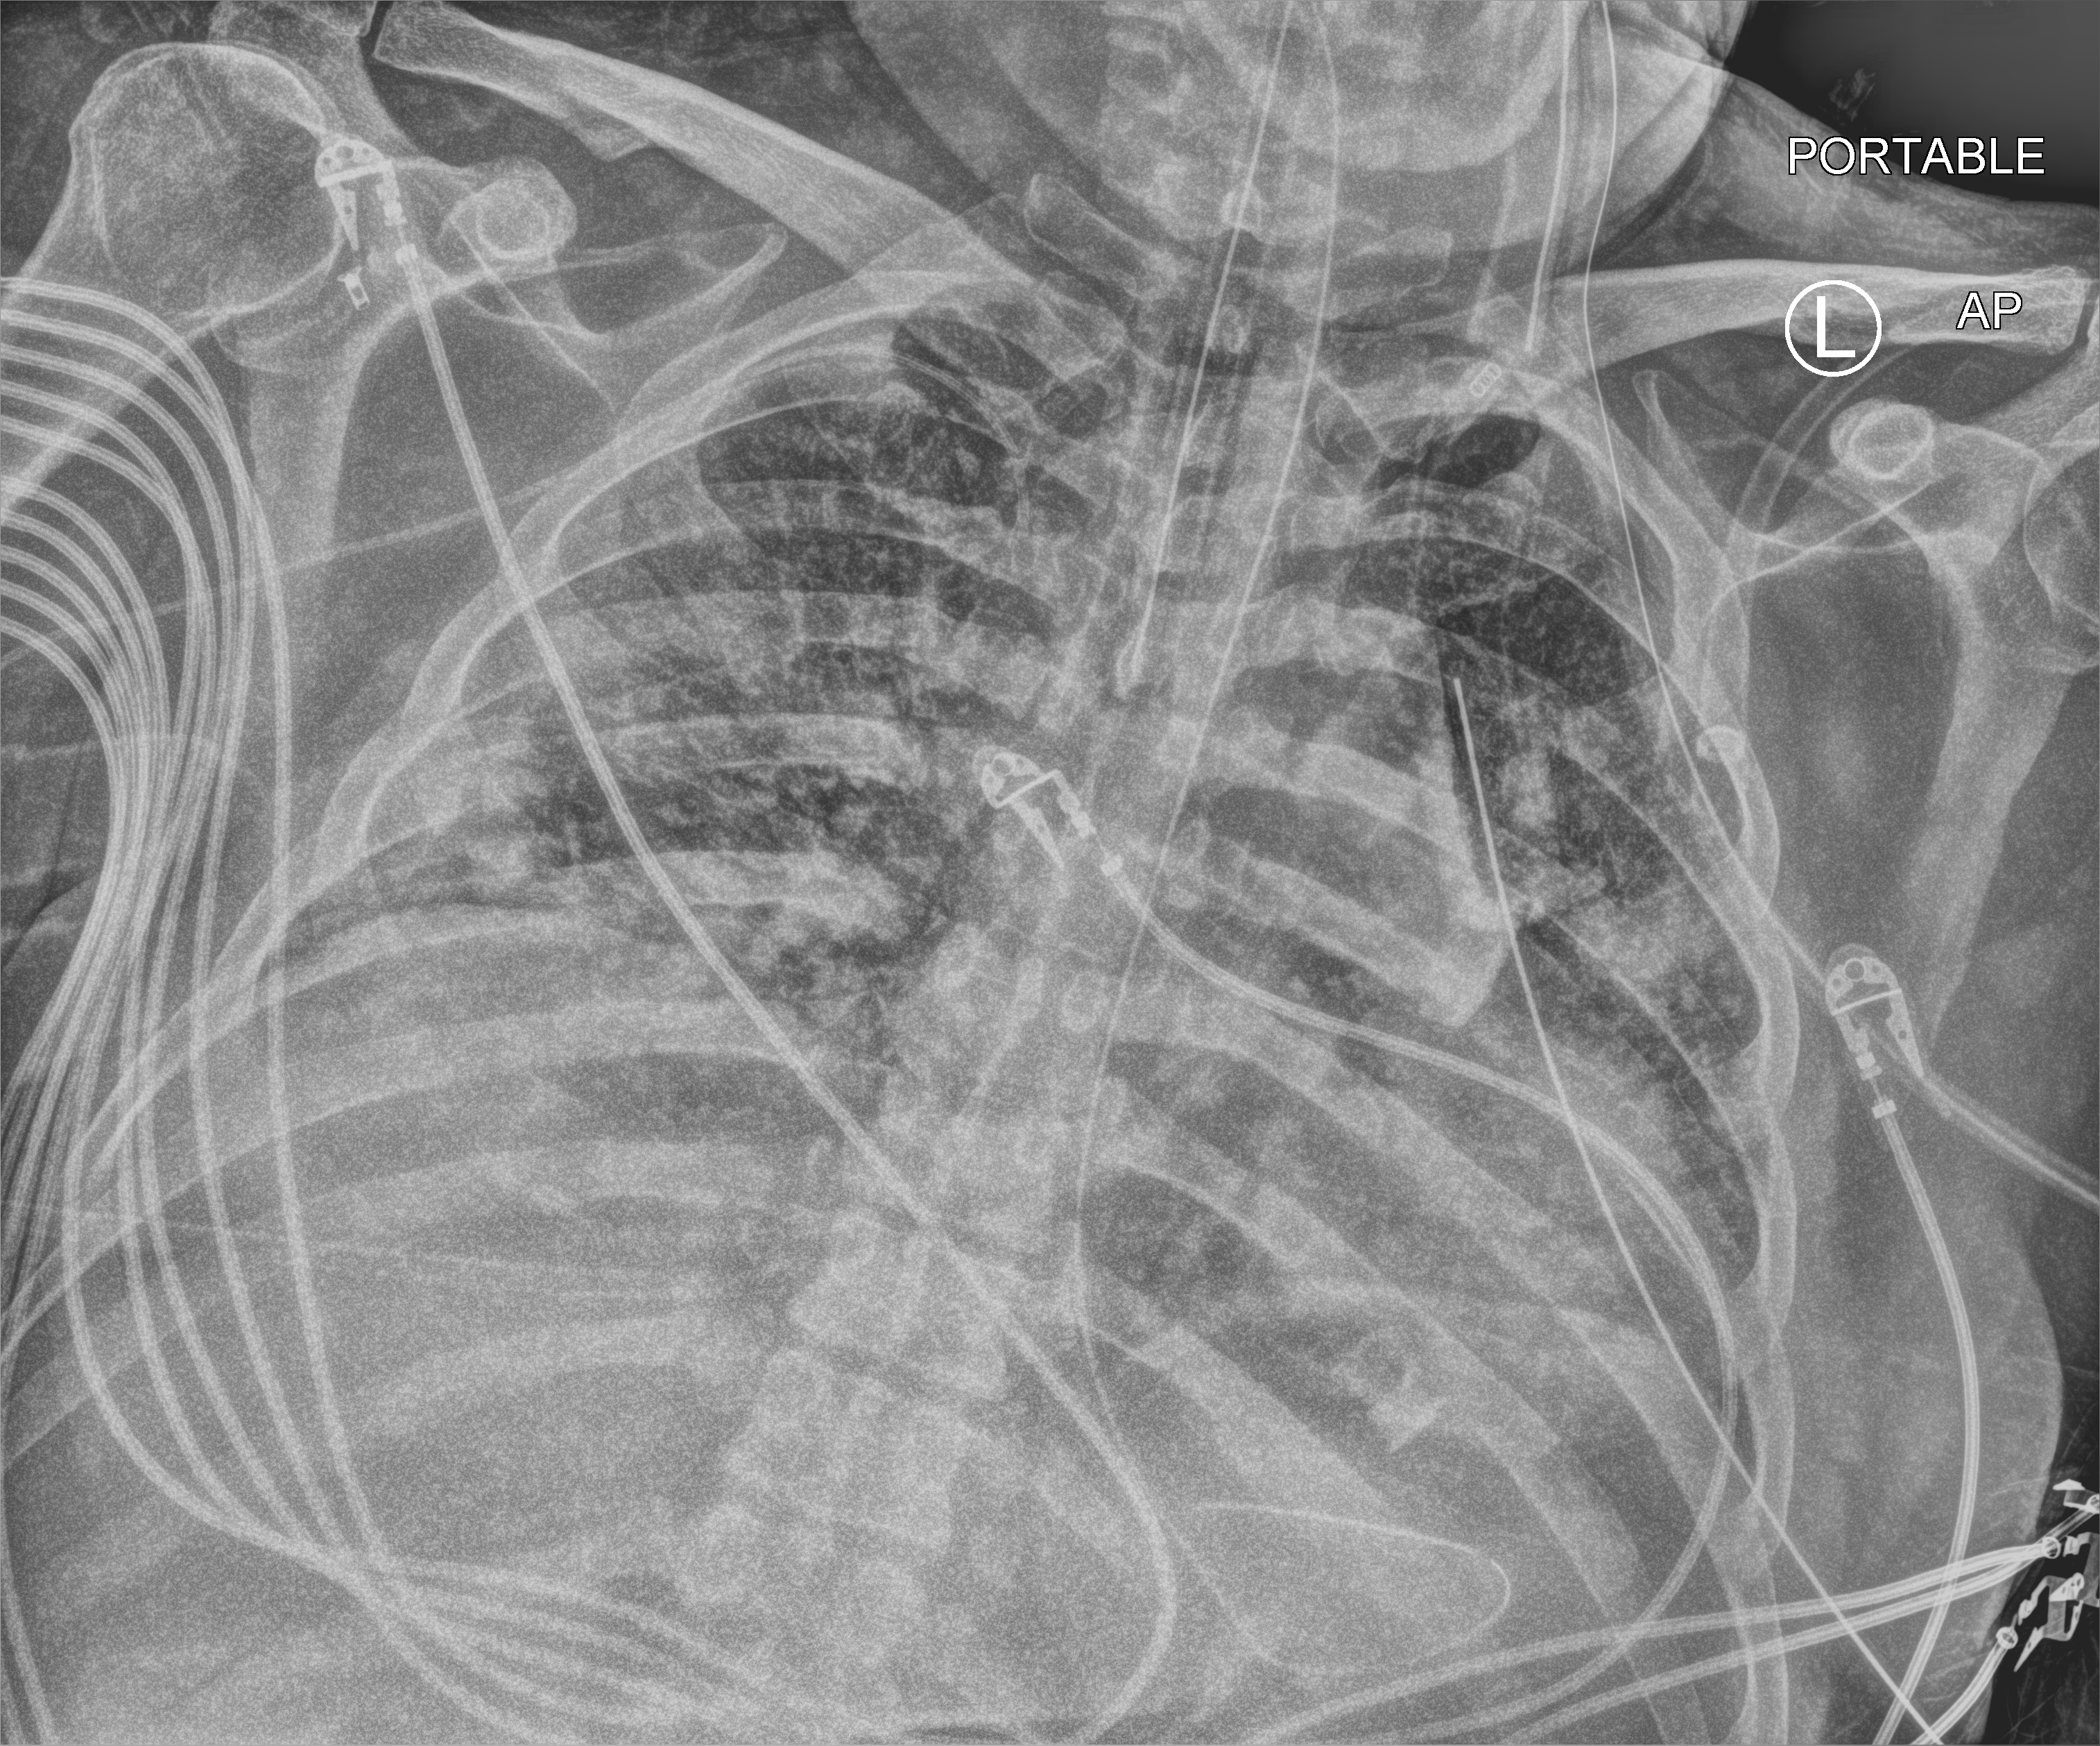
Chest X-ray (portable). Patient hospitalised with COVID-19; male, aged 18–59 years.
Admission-level facts for this patient (not findings on this image; timing relative to this image not recorded):
- diabetes (admission record): no